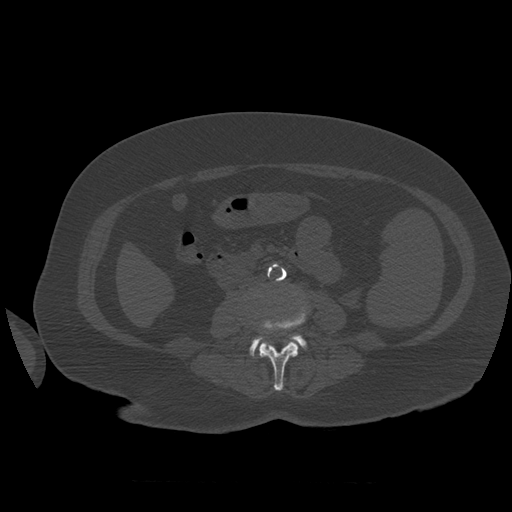
CT including the spine, one axial slice. Slice 221 of 399 in the series (ordered by position). Reconstruction kernel STANDARD. 120 kVp. Bone window (W 1800 / L 400 HU). 512 × 512 image matrix, field of view 404 × 404 mm. Patient age 81 years. From the clinical record (not read from this slice): primary cancer: renal; vertebrae with lytic lesions (as recorded): L1.
Outlined on this slice (semi-automatic segmentation, software-assisted and operator-edited):
- L3 vertebra: bounding box [x1, y1, x2, y2] px = [257, 300, 307, 391]
- L4 vertebra: [249, 335, 307, 357]